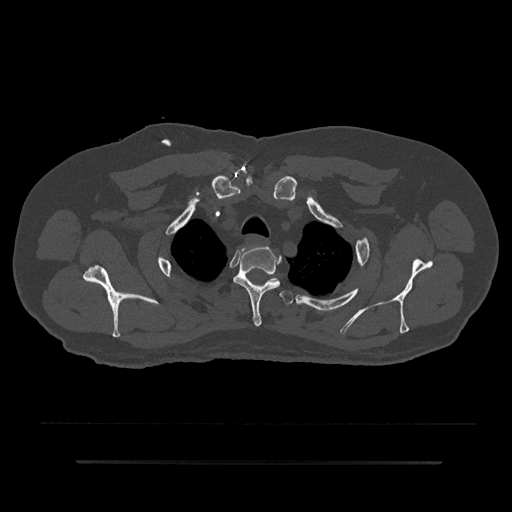
CT including the spine, one axial slice. Position 692 of 797 along the scan axis. Reconstruction kernel Br40s/3. Bone window (W 1800 / L 400 HU). 0.5 mm slice thickness. 512 × 512 image matrix. Patient: male, 59 years. From the clinical record (not read from this slice): primary cancer: bile ducts; vertebrae with lytic lesions (as recorded): T10.
Outlined on this slice (semi-automatically segmented with operator editing):
- T2 vertebra: bounding box (x1, y1, x2, y2) in pixels: (233, 246, 281, 327)
- T3 vertebra: (279, 291, 293, 305)